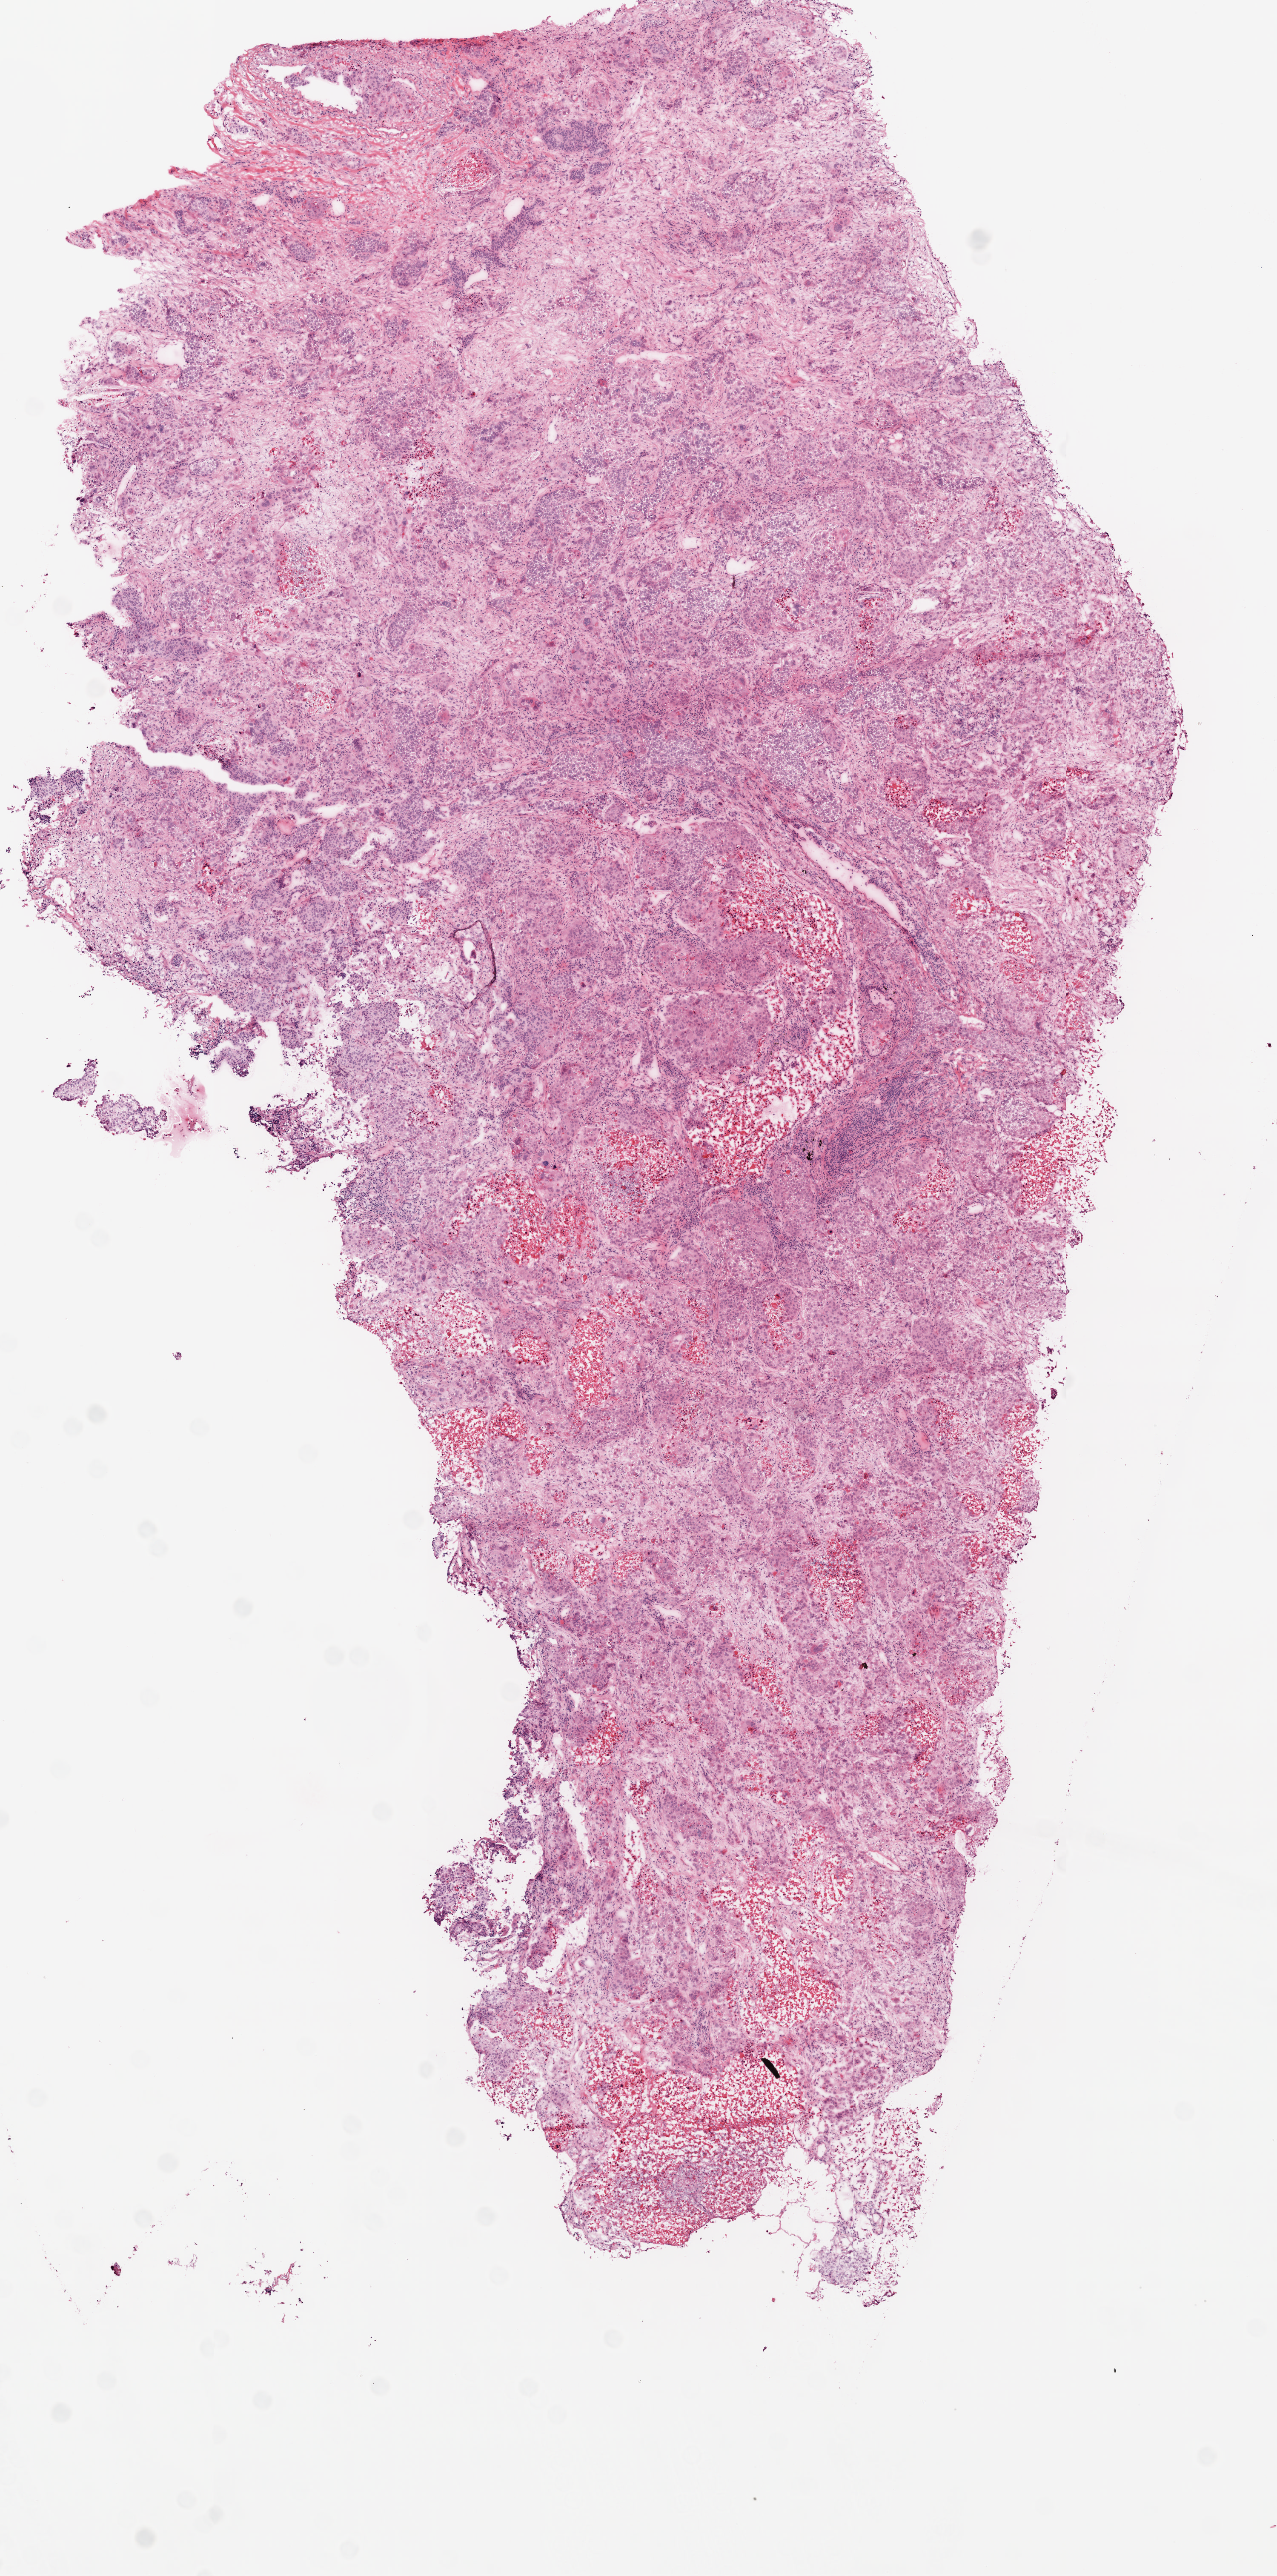
Whole-slide histology image, Hematoxylin and eosin (H&E) stained — whole scanned area (about 6.0 x 12.1 mm) shown as a low-resolution overview, frozen section from the top of the tissue portion, primary tumour sample from the lung. Male, age 57 years at initial diagnosis. Composition of this section per pathologist review: tumour cells 60%, tumour nuclei 70%, normal cells 0%, stromal cells 25%, necrosis 15%.
• AJCC pathologic stage: IIIA
• histologic diagnosis: Squamous cell carcinoma, NOS (lower lobe, lung)